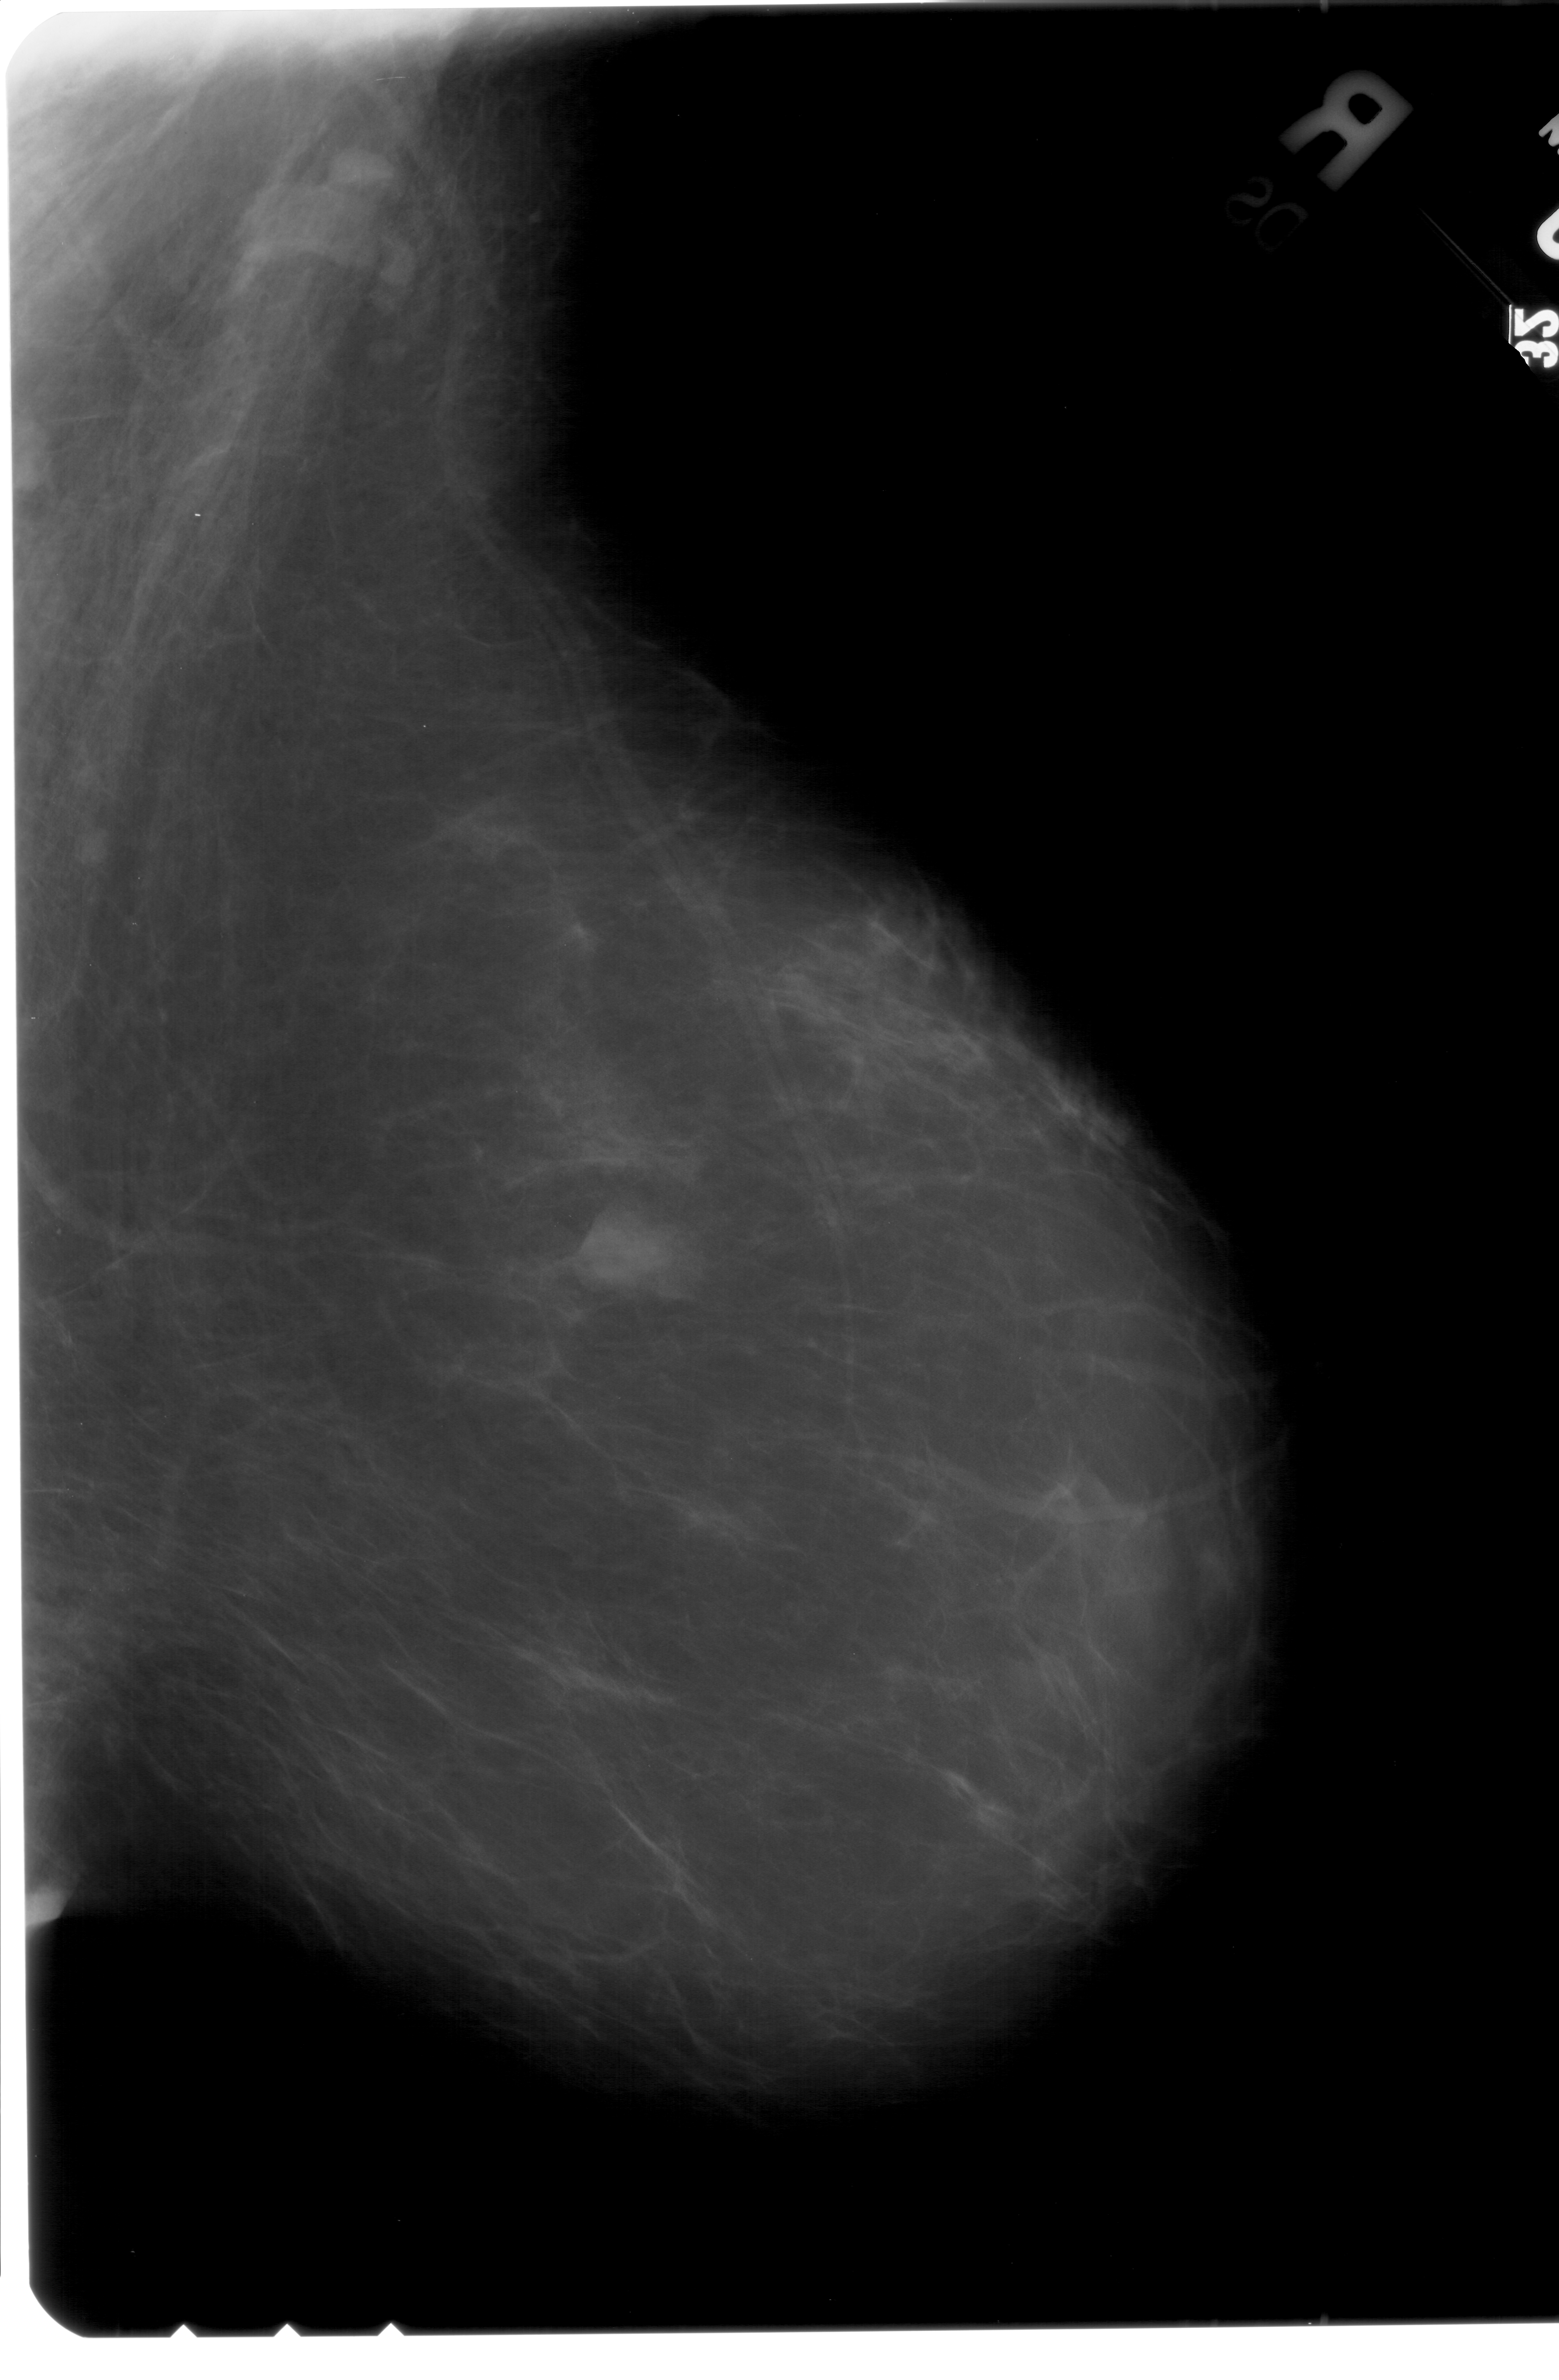
Scanned film-screen mammogram; right breast; mediolateral oblique (MLO) view; breast composition: scattered fibroglandular densities (BI-RADS density category 2 of 4).
- Radiologist-marked abnormalities on this image: mass, shape lobulated, margins circumscribed; BI-RADS assessment category 4; subtlety rating 4 on a 1 (subtle) to 5 (obvious) scale; pathology (as recorded): benign.